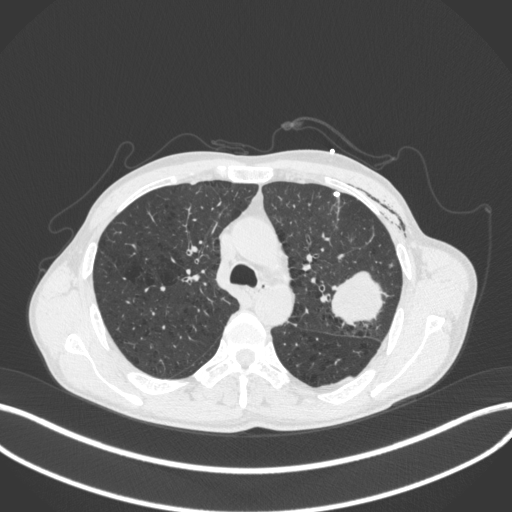
Chest CT, one axial slice; 120 kVp; lung window (W 1500 / L -600 HU); 1 mm slice thickness; 512 × 512 image matrix, field of view 400 × 400 mm. Male patient, age 58 years. From the clinical record (not read from this slice): clinical TNM (as recorded): T3 N0 M0.
Annotated regions visible in this slice (bounding box drawn by a radiologist):
- lung tumour (recorded histology: adenocarcinoma): bounding box (x1, y1, x2, y2) in pixels: (323, 263, 388, 329)